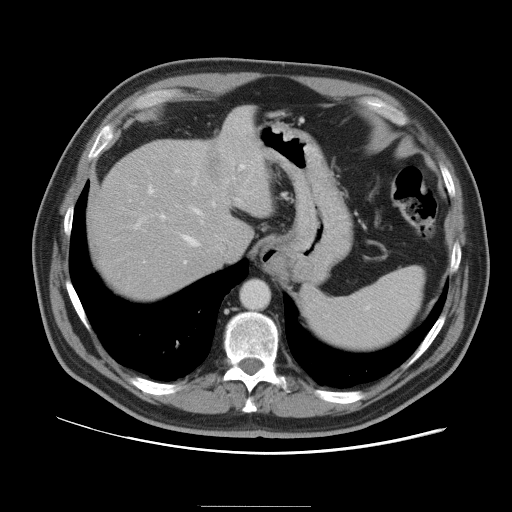
Contrast-enhanced abdominal CT, one axial slice. 120 kVp. Intravenous contrast given. Soft-tissue window (W 400 / L 40 HU). 5 mm slice thickness. 512 × 512 image matrix, field of view 399 × 399 mm. Male patient, age 64 years. From the clinical record (not read from this slice): diagnosis: colorectal cancer liver metastases, imaged before liver resection; multiple liver metastases: yes; largest metastasis: 3 cm.
Outlined on this slice (outlined manually by an expert reader):
- hepatic veins: bounding box <182,206,203,246> (left, top, right, bottom; pixels)
- liver: <90,108,270,299>
- planned liver remnant (the part of the liver to remain after resection): <91,147,230,299>
- portal vein (with intrahepatic branches): <134,165,245,264>
- liver metastasis: <209,158,220,178>